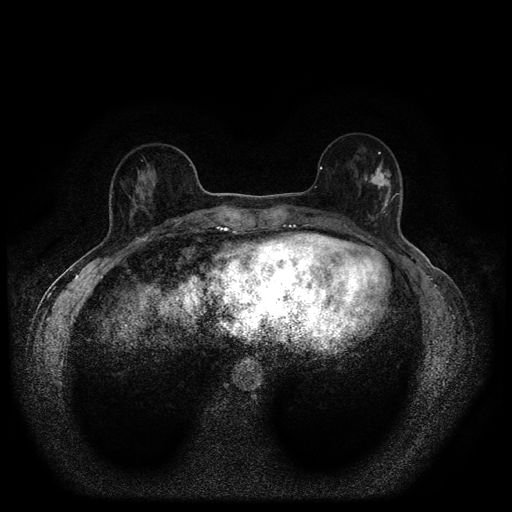
Breast MRI (dynamic contrast-enhanced, multi-phase), one axial slice. Slice 36 of 116 in the series (ordered by position). Dynamic contrast-enhanced series, time point 2 of 5 at this slice position (early post-contrast). 1.5 T. TE 2.7 ms, TR 5.4 ms. 2 mm slice thickness. 512 × 512 image matrix, field of view 330 × 330 mm. Patient: female, 56 years.
Structures marked on this image (semi-automatic segmentation, software-assisted and operator-edited):
- breast lesion (labelled 'tumour' in the annotation; benign lesions carry a separate 'benign' label): bounding box [x1, y1, x2, y2] px = [364, 158, 394, 217]